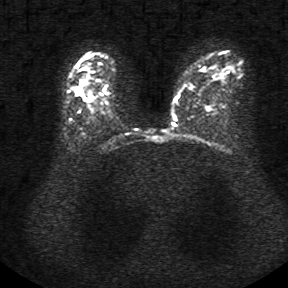
Breast MRI, one axial slice; position 26 of 34 along the scan axis; diffusion-weighted series; image 2 of 4 stored at this slice position (different b-values; order by instance number); 1.5 T; 288 × 288 image matrix. Female patient.
Annotated regions visible in this slice (expert manual segmentation):
- tumour on diffusion-weighted imaging: box from (x=77, y=86) to (x=82, y=95) px